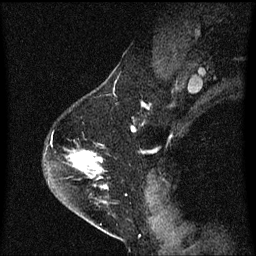
Breast MRI (dynamic contrast-enhanced), one sagittal slice; slice 44 of 60 in the series (ordered by position); dynamic contrast-enhanced series, image 2 of 3 at this slice position (ordered by acquisition); 1.5 T; TE 4.2 ms, TR 8.4 ms; 2 mm slice thickness; 256 × 256 image matrix. Female patient, age 54 years. From the clinical record (not read from this slice): setting: breast cancer imaged before/during neoadjuvant chemotherapy; receptor status: HER2-positive.
Annotated regions visible in this slice (semi-automatically segmented with operator editing):
- analysis volume of interest (the breast-tissue region the enhancement analysis was run in; not a lesion): box from (x=46, y=140) to (x=111, y=213) px
- tumour enhancement mask (voxels above the 70 % enhancement threshold inside the analysis volume of interest): (x=72, y=154)–(x=99, y=169)